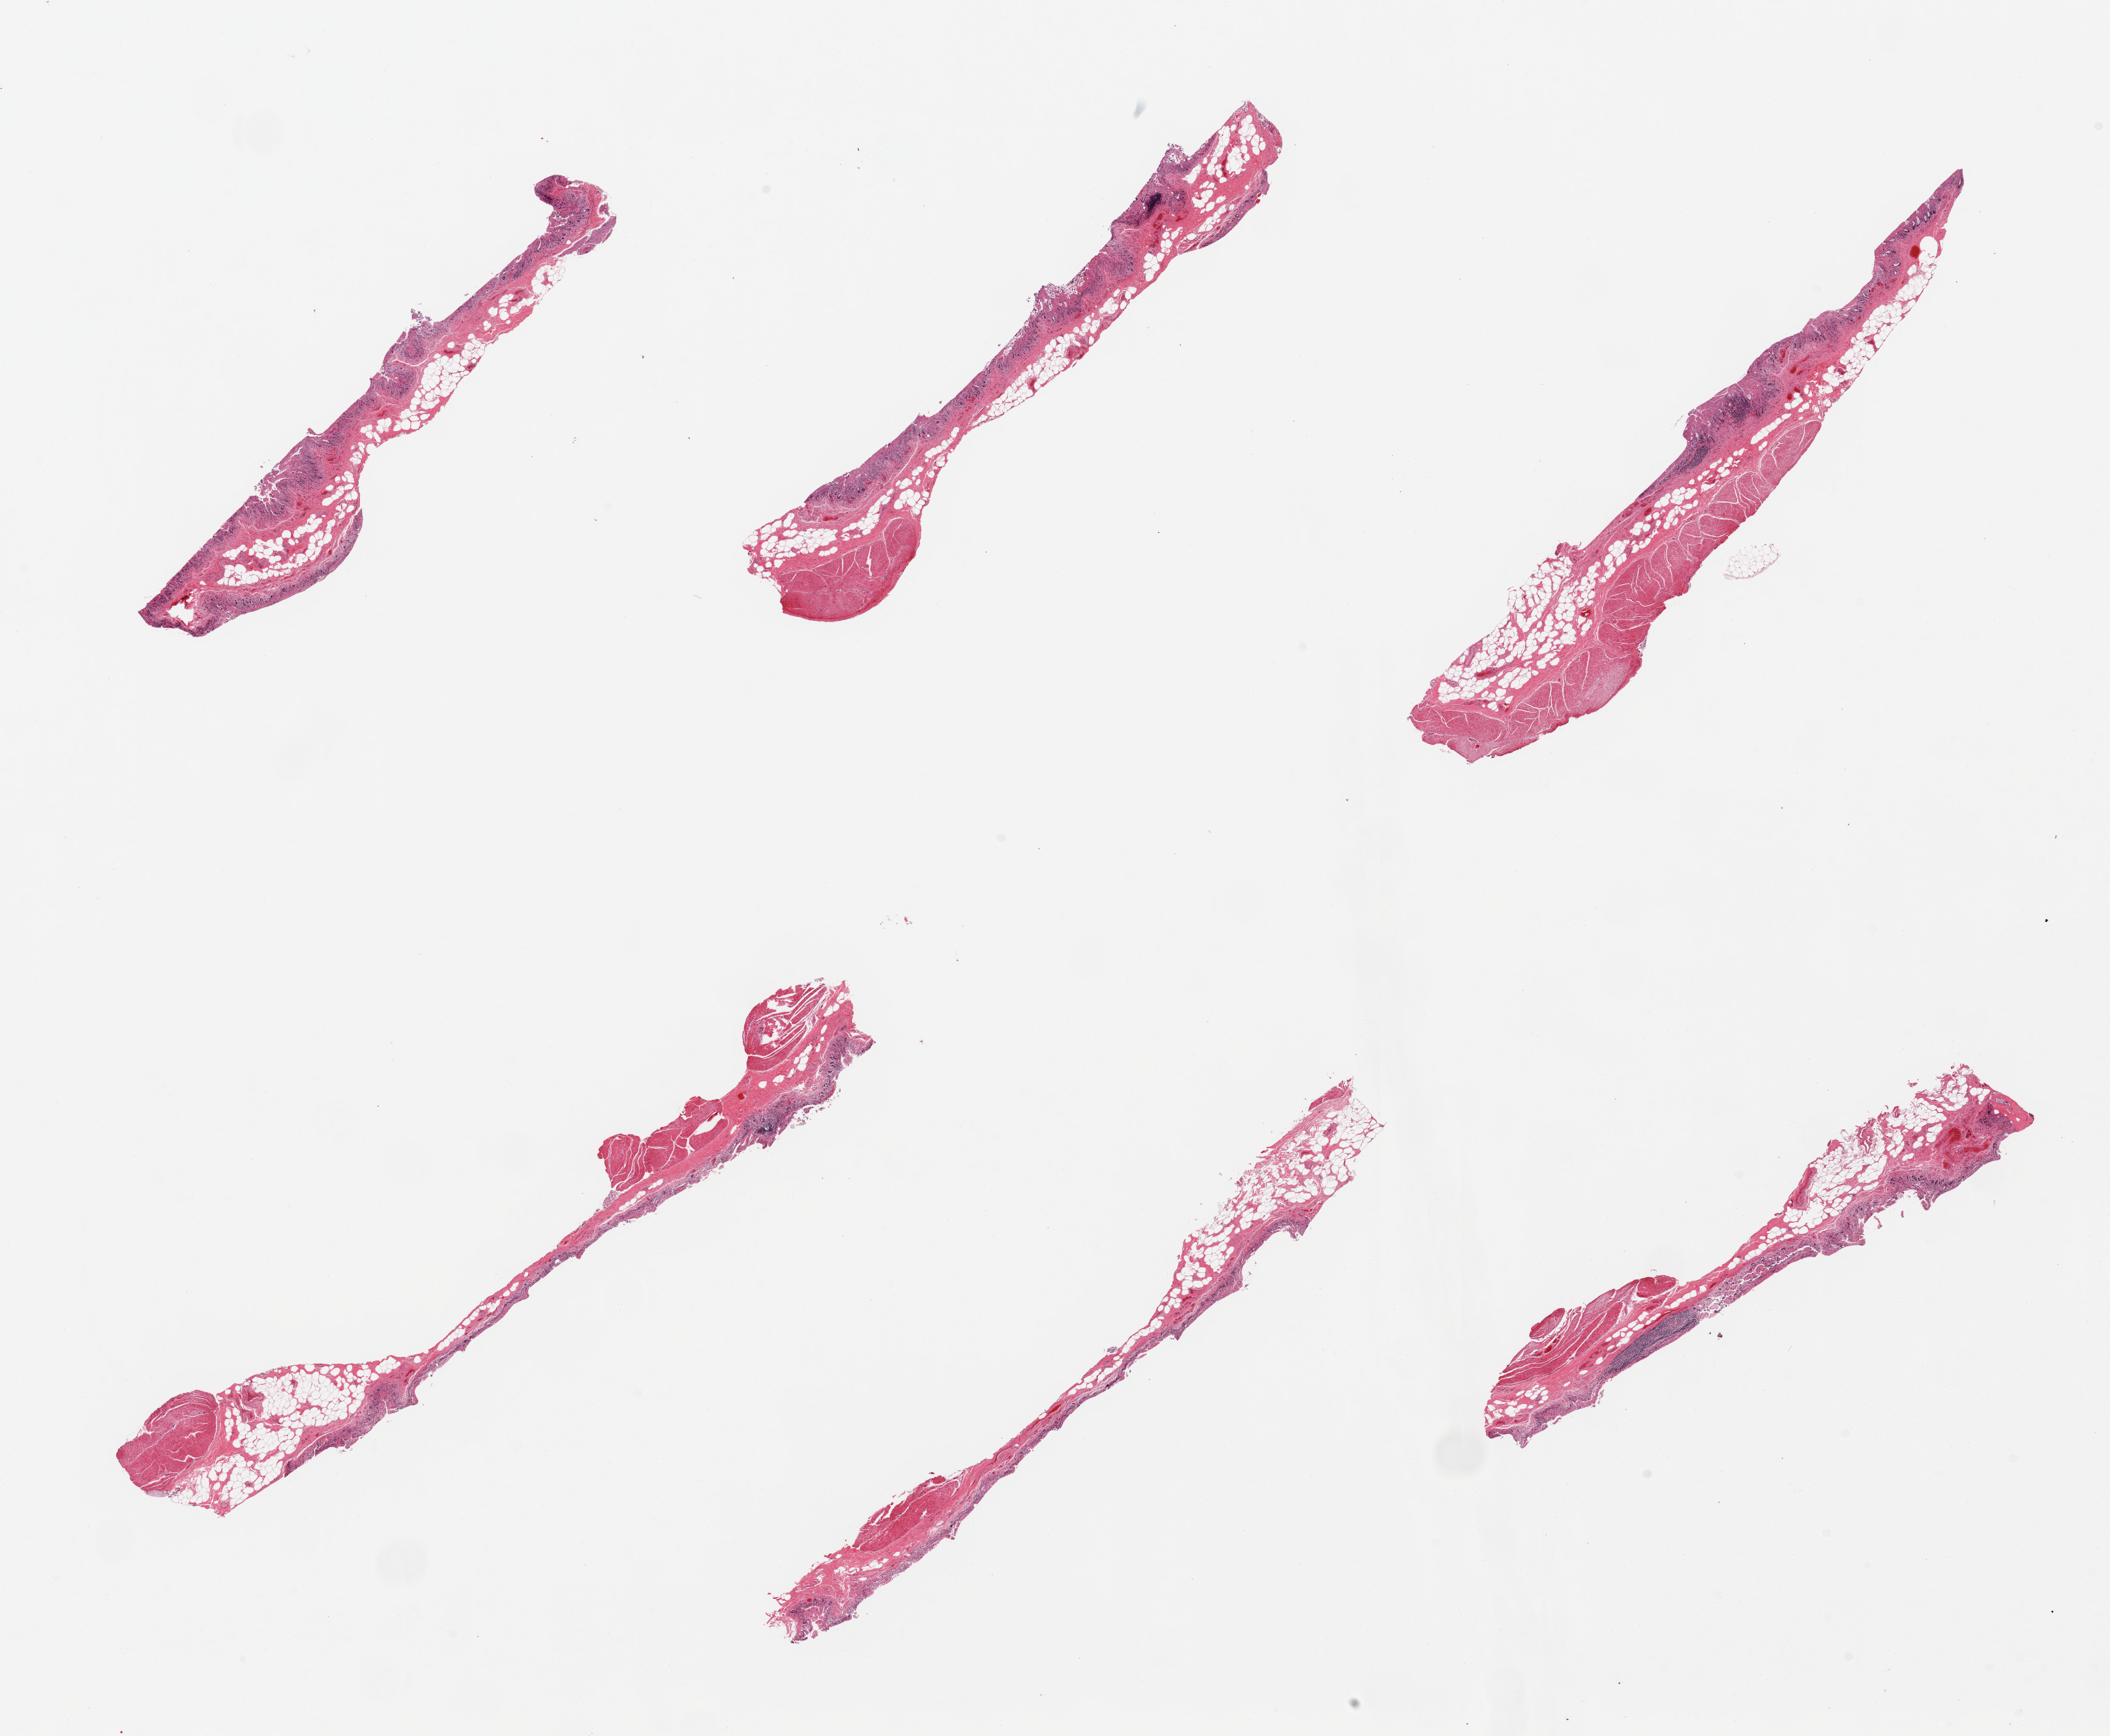
Digitized H&E-stained section, shown as a low-resolution overview of the whole scanned area (about 25.6 x 21.1 mm, acquisition: 20x scan). Donor: male.
Specimen: PAXgene-fixed, paraffin-embedded tissue; target tissue: ileum; tissue donor sample.